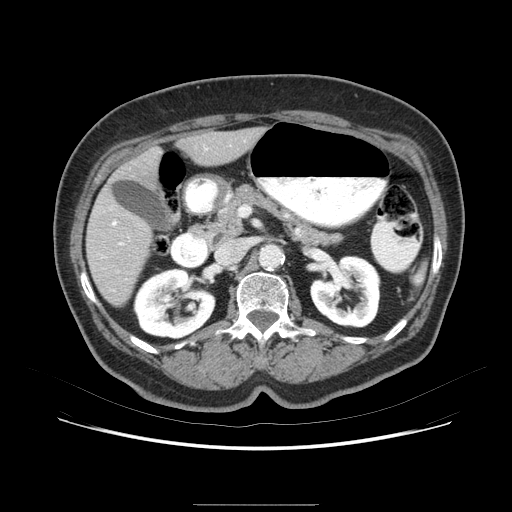
Contrast-enhanced abdominal CT (liver protocol), one axial slice; slice 32 of 79 in the series (ordered by position); soft-tissue window (W 400 / L 40 HU); 512 × 512 image matrix, field of view 380 × 380 mm. From the clinical record (not read from this slice): diagnosis: hepatocellular carcinoma (patient treated with transarterial chemoembolisation; whether this scan precedes or follows treatment is not stated here); TNM stage (as recorded): Stage-I; Child-Pugh class: A; tumour differentiation: poorly differentiated; tumour nodularity: uninodular.
Annotated regions visible in this slice (semi-automatic segmentation, software-assisted and operator-edited):
- liver parenchyma outside the tumour (the mass and vessels are separate outlines, so this box may not span the whole liver): bounding box <84,122,272,320> (left, top, right, bottom; pixels)
- mass: <104,188,150,230>
- liver vessels: <123,150,238,274>